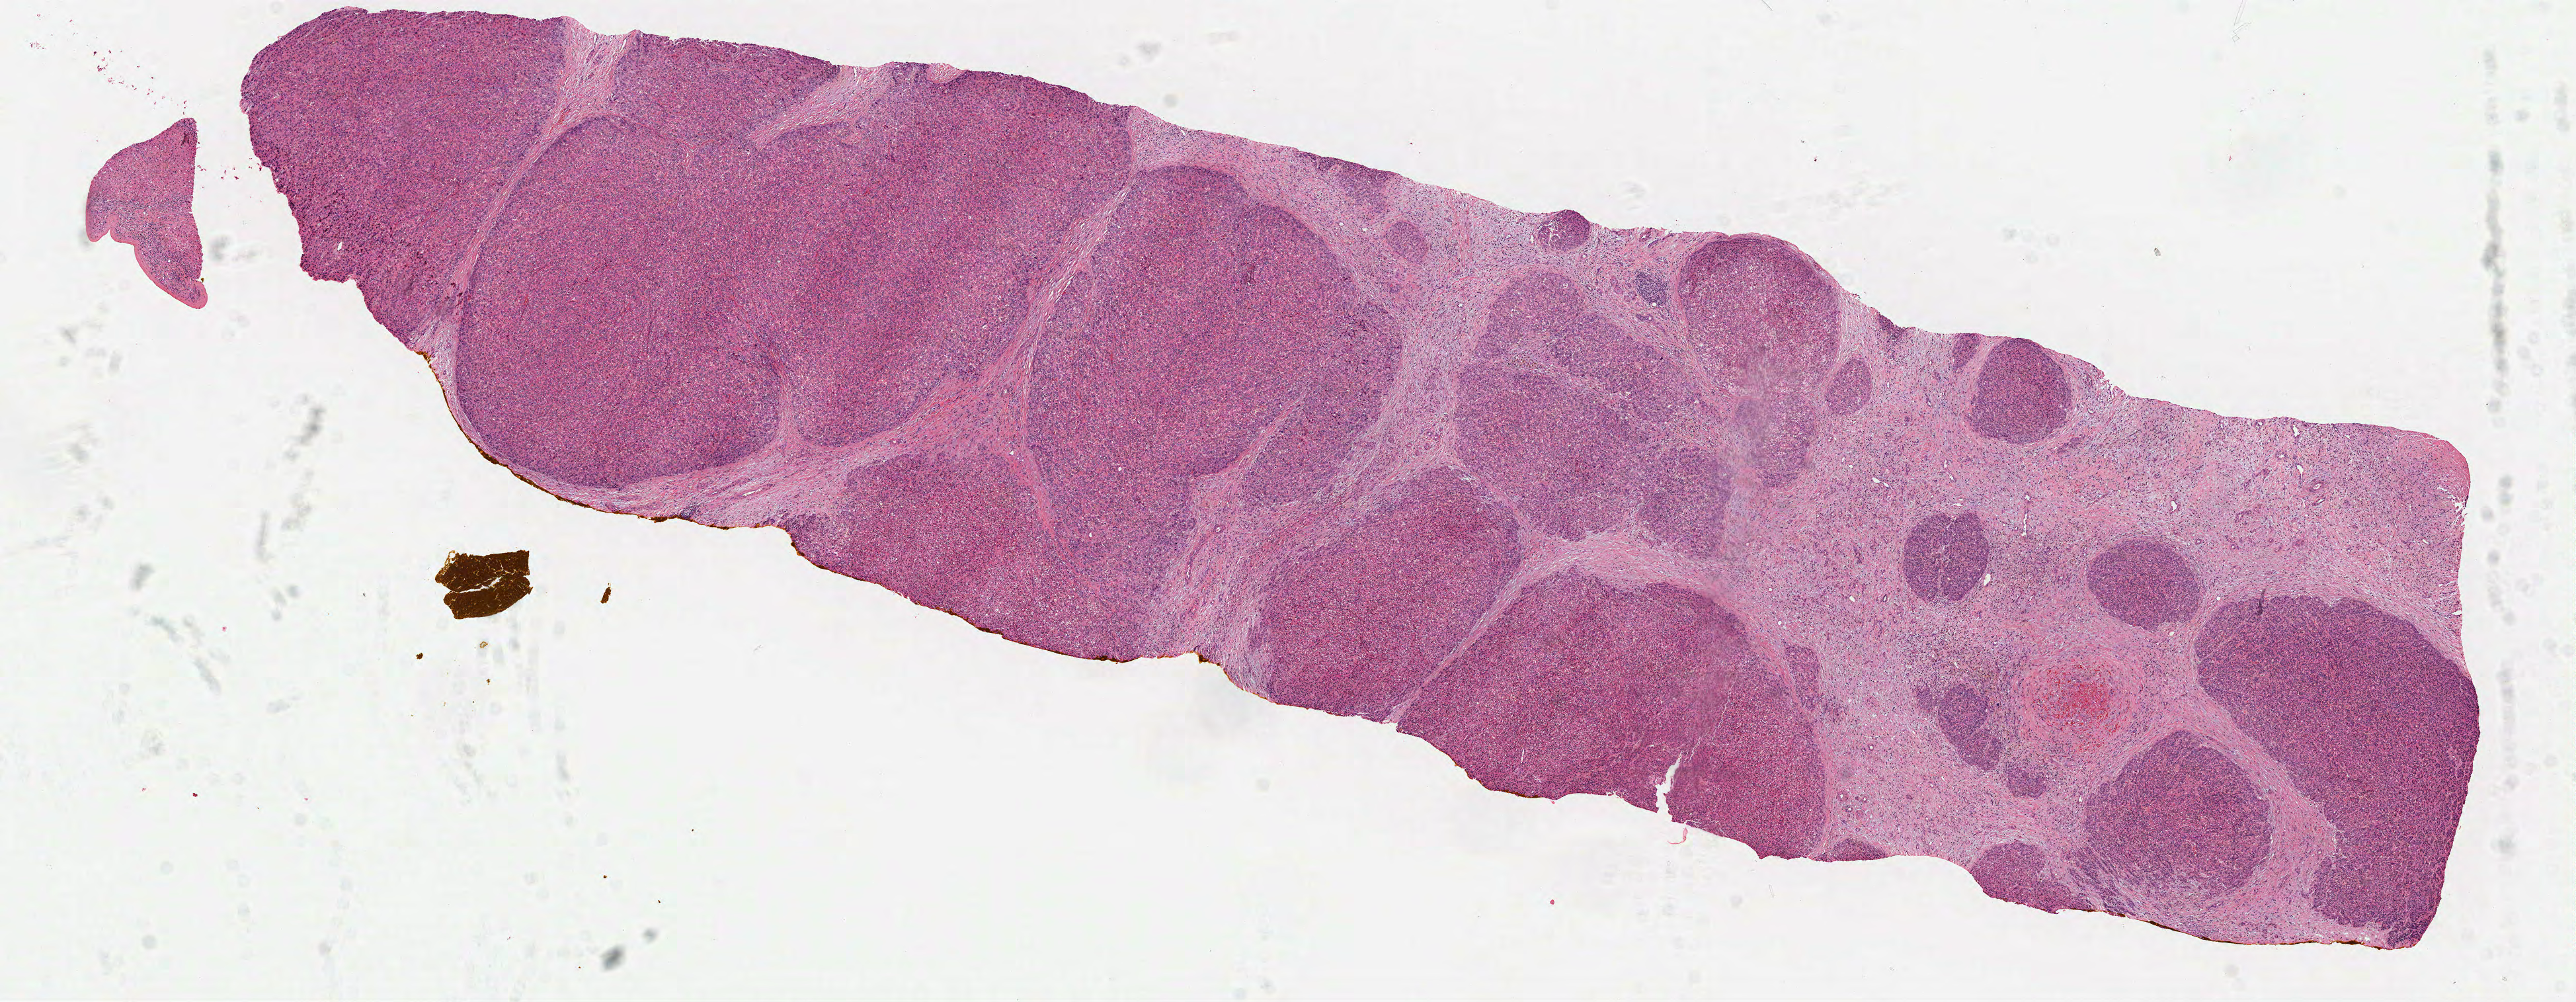
Digitized Hematoxylin and eosin (H&E) stained tissue section (whole slide) — a low-resolution overview of the entire scanned area, about 15.7 x 6.1 mm. Formalin-fixed paraffin-embedded (FFPE) diagnostic section. Liver, primary tumour sample. Female, age 51 years at initial diagnosis.
Pathologic diagnosis: Hepatocellular carcinoma, NOS.